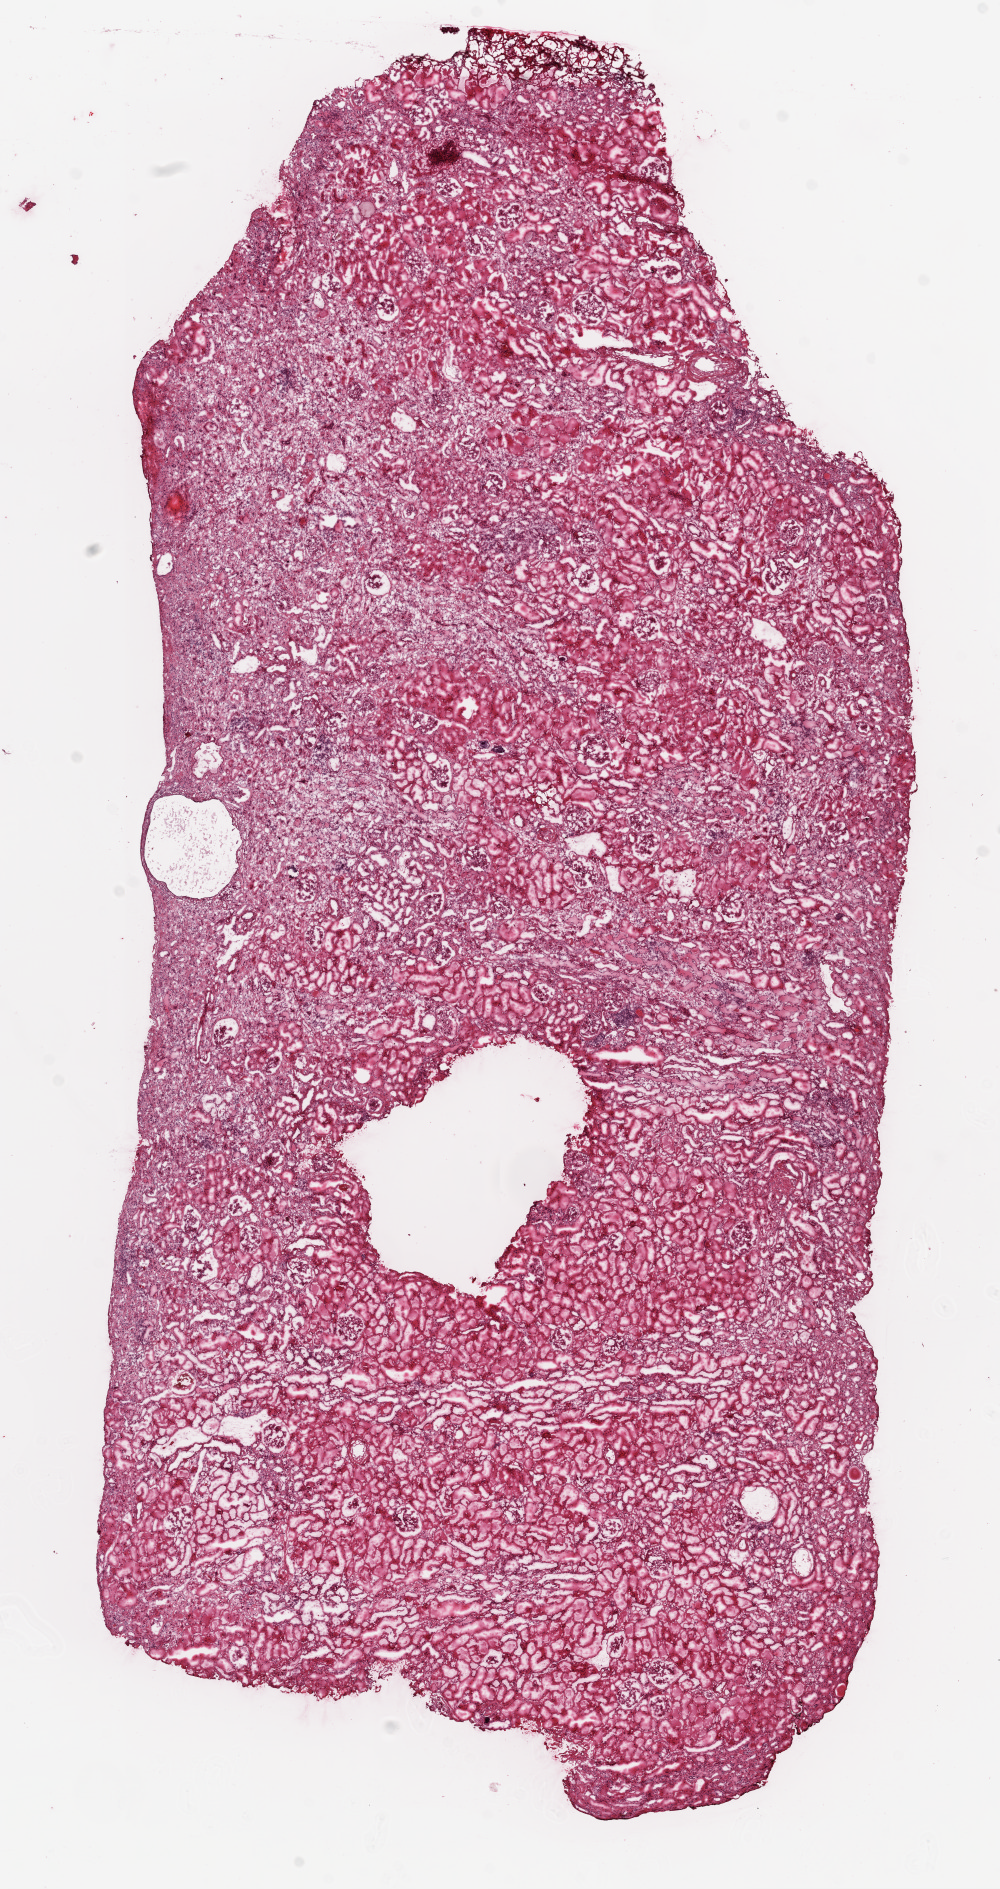
Digitized H&E tissue section (whole slide) — a low-resolution overview of the entire scanned area, about 8.0 x 15.2 mm. Frozen section. Solid tissue normal (non-tumour tissue) sample from the kidney. Male, age 75 years at initial diagnosis.
* this section: solid tissue normal sample (biorepository sample class)
* patient diagnosis: Clear cell adenocarcinoma, NOS